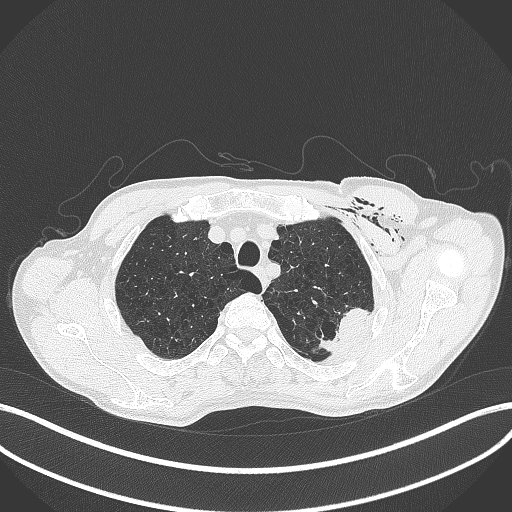
Chest CT, one axial slice. Slice 350 of 457 in the series (ordered by position). Reconstruction kernel B70f. Lung window (W 1500 / L -600 HU). 1 mm slice thickness. 512 × 512 image matrix, field of view 400 × 400 mm. Patient: male, 58 years. From the clinical record (not read from this slice): clinical TNM (as recorded): T3 N0 M0.
Structures marked on this image (bounding box drawn by a radiologist):
- lung tumour (recorded histology: adenocarcinoma): bounding box [x1, y1, x2, y2] px = [314, 302, 370, 357]